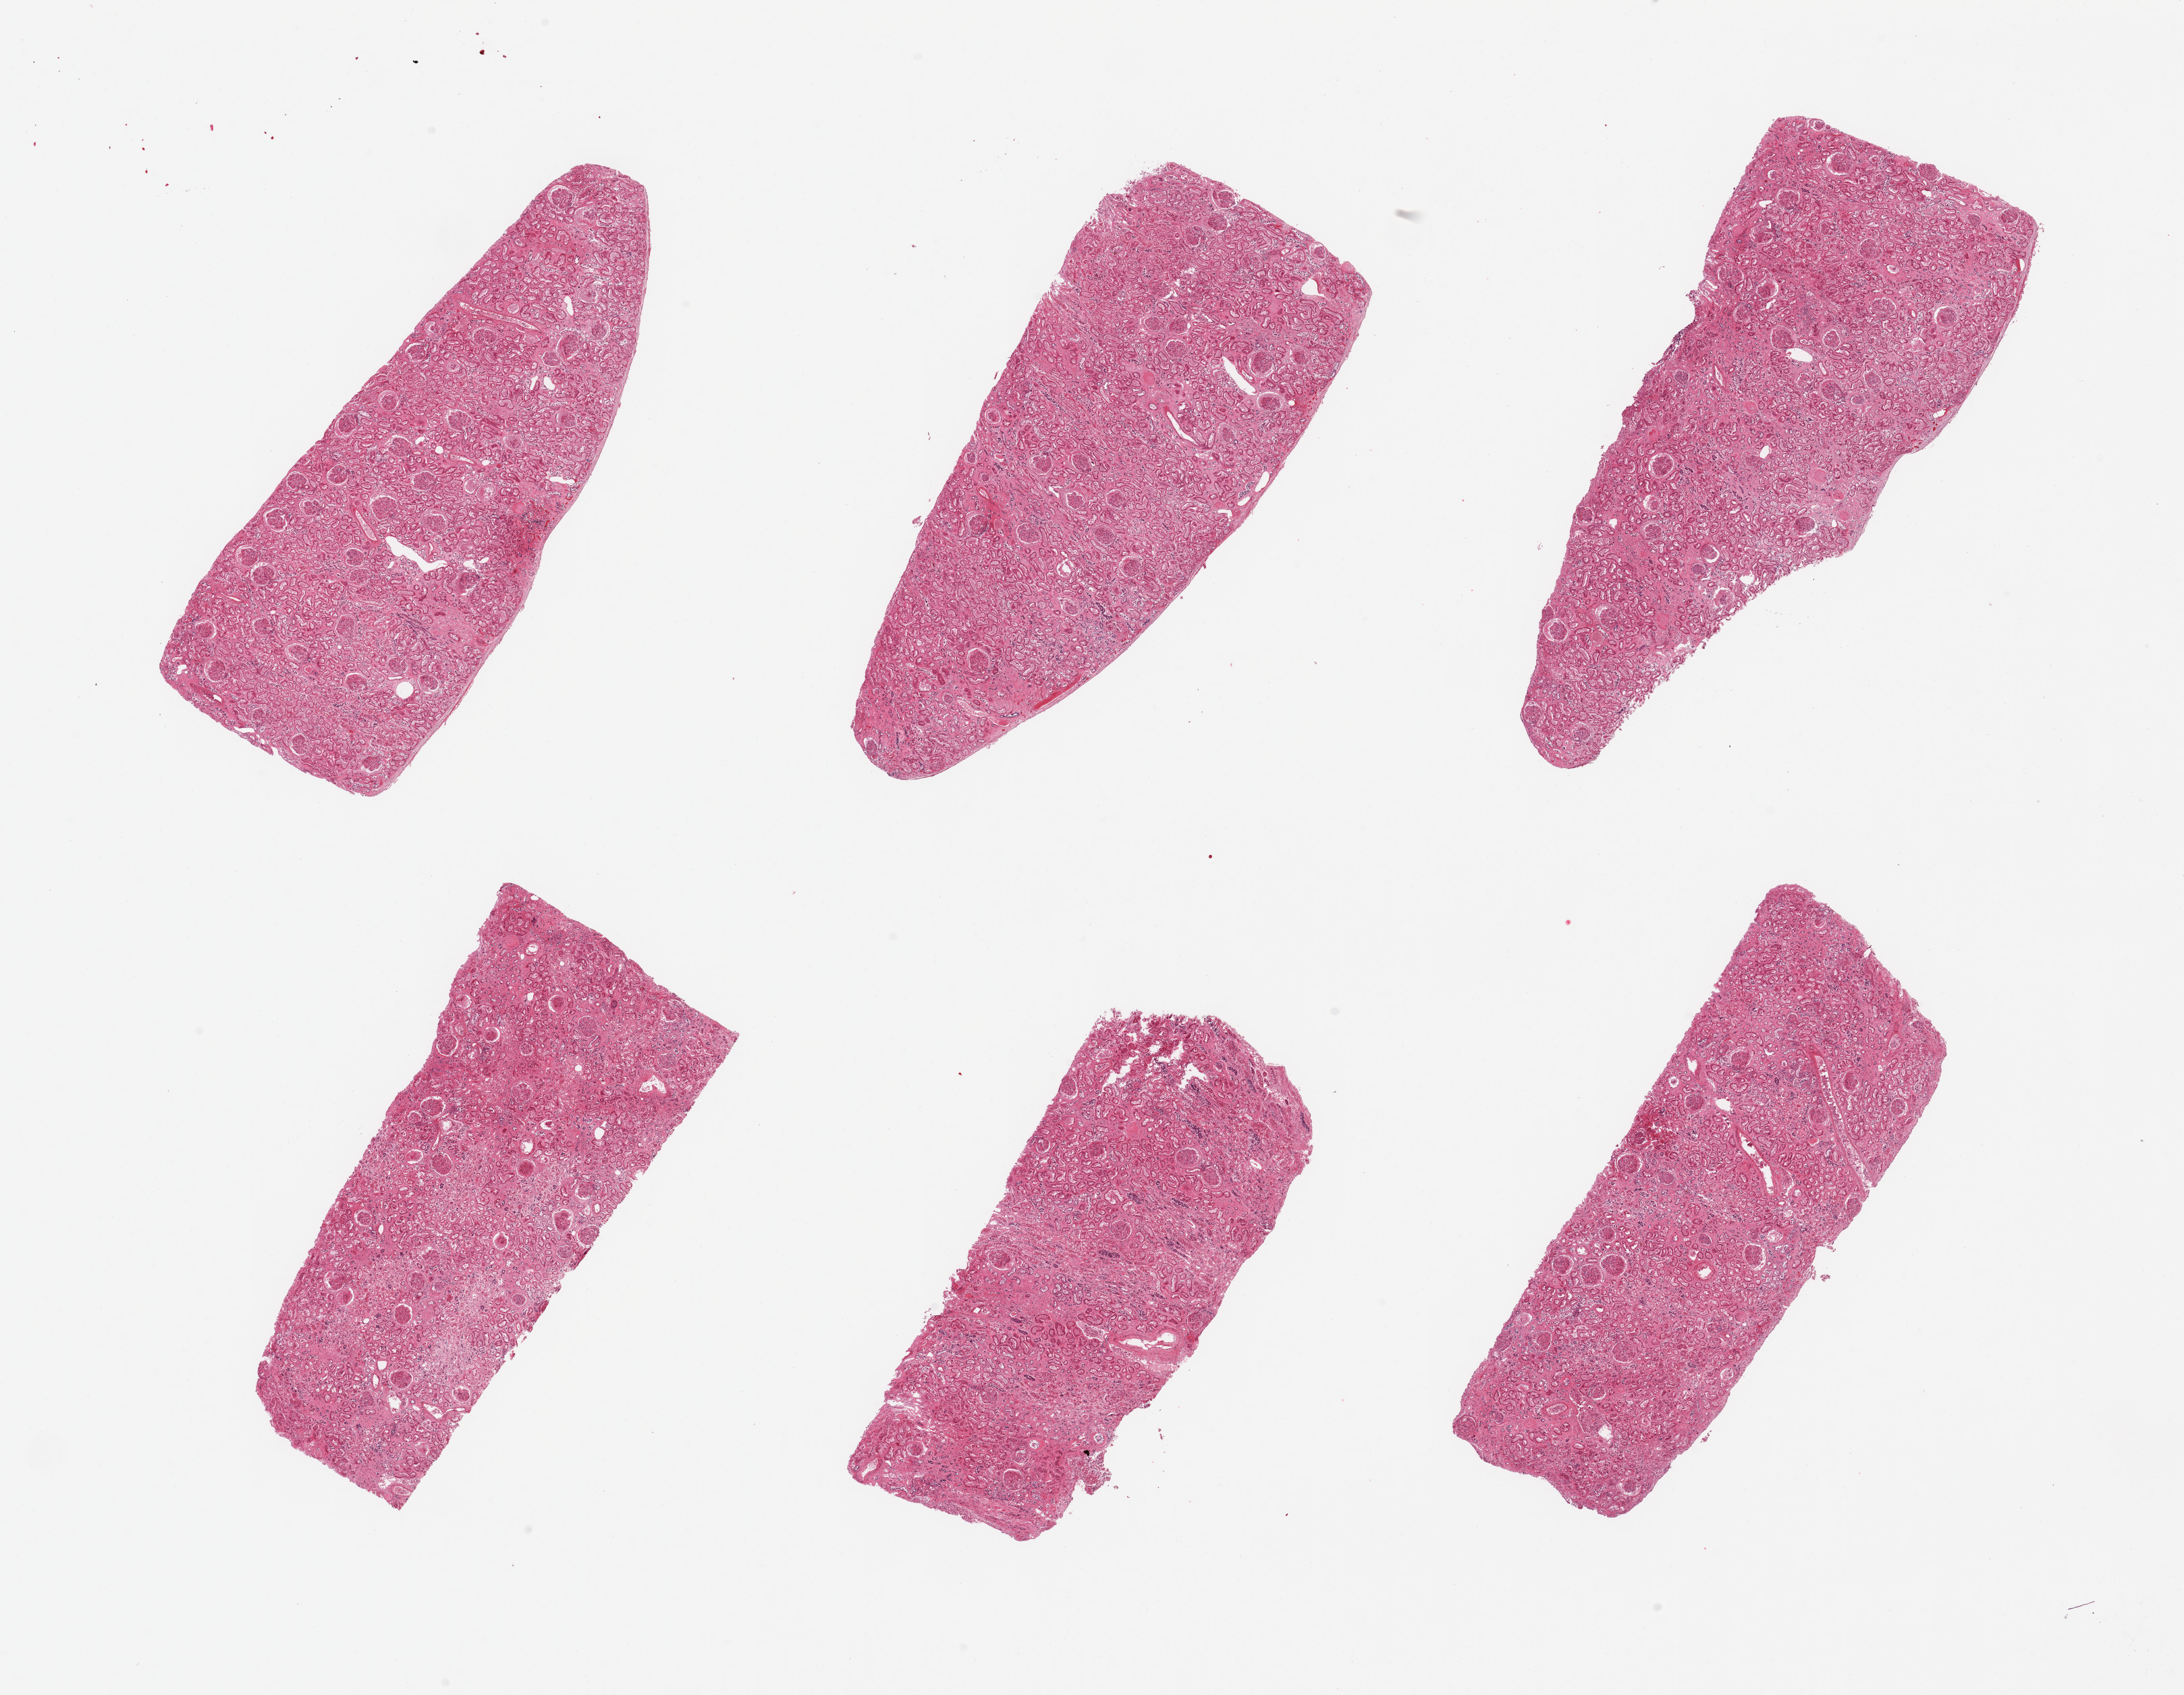
Digitized hematoxylin and eosin (H&E)-stained section, shown as a low-resolution overview of the whole scanned area (about 25.6 x 19.9 mm), PAXgene-fixed, paraffin-embedded tissue, target tissue: renal cortex, donor tissue sample. Donor: male.
- review note (as recorded): 6 pieces, glomeruli present; tubules with advanced autolysis